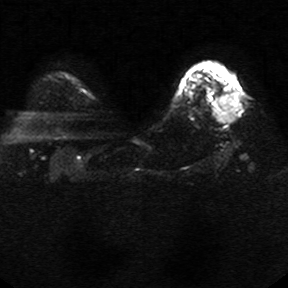
Breast MRI, one axial slice; slice 21 of 34 in the series (ordered by position); diffusion-weighted series; image 2 of 4 stored at this slice position (different b-values; order by instance number); 1.5 T; 5 mm slice thickness; 288 × 288 image matrix. Female patient.
Annotated regions visible in this slice (outlined manually by an expert reader):
- tumour on diffusion-weighted imaging: bounding box <215,92,241,123> (left, top, right, bottom; pixels)